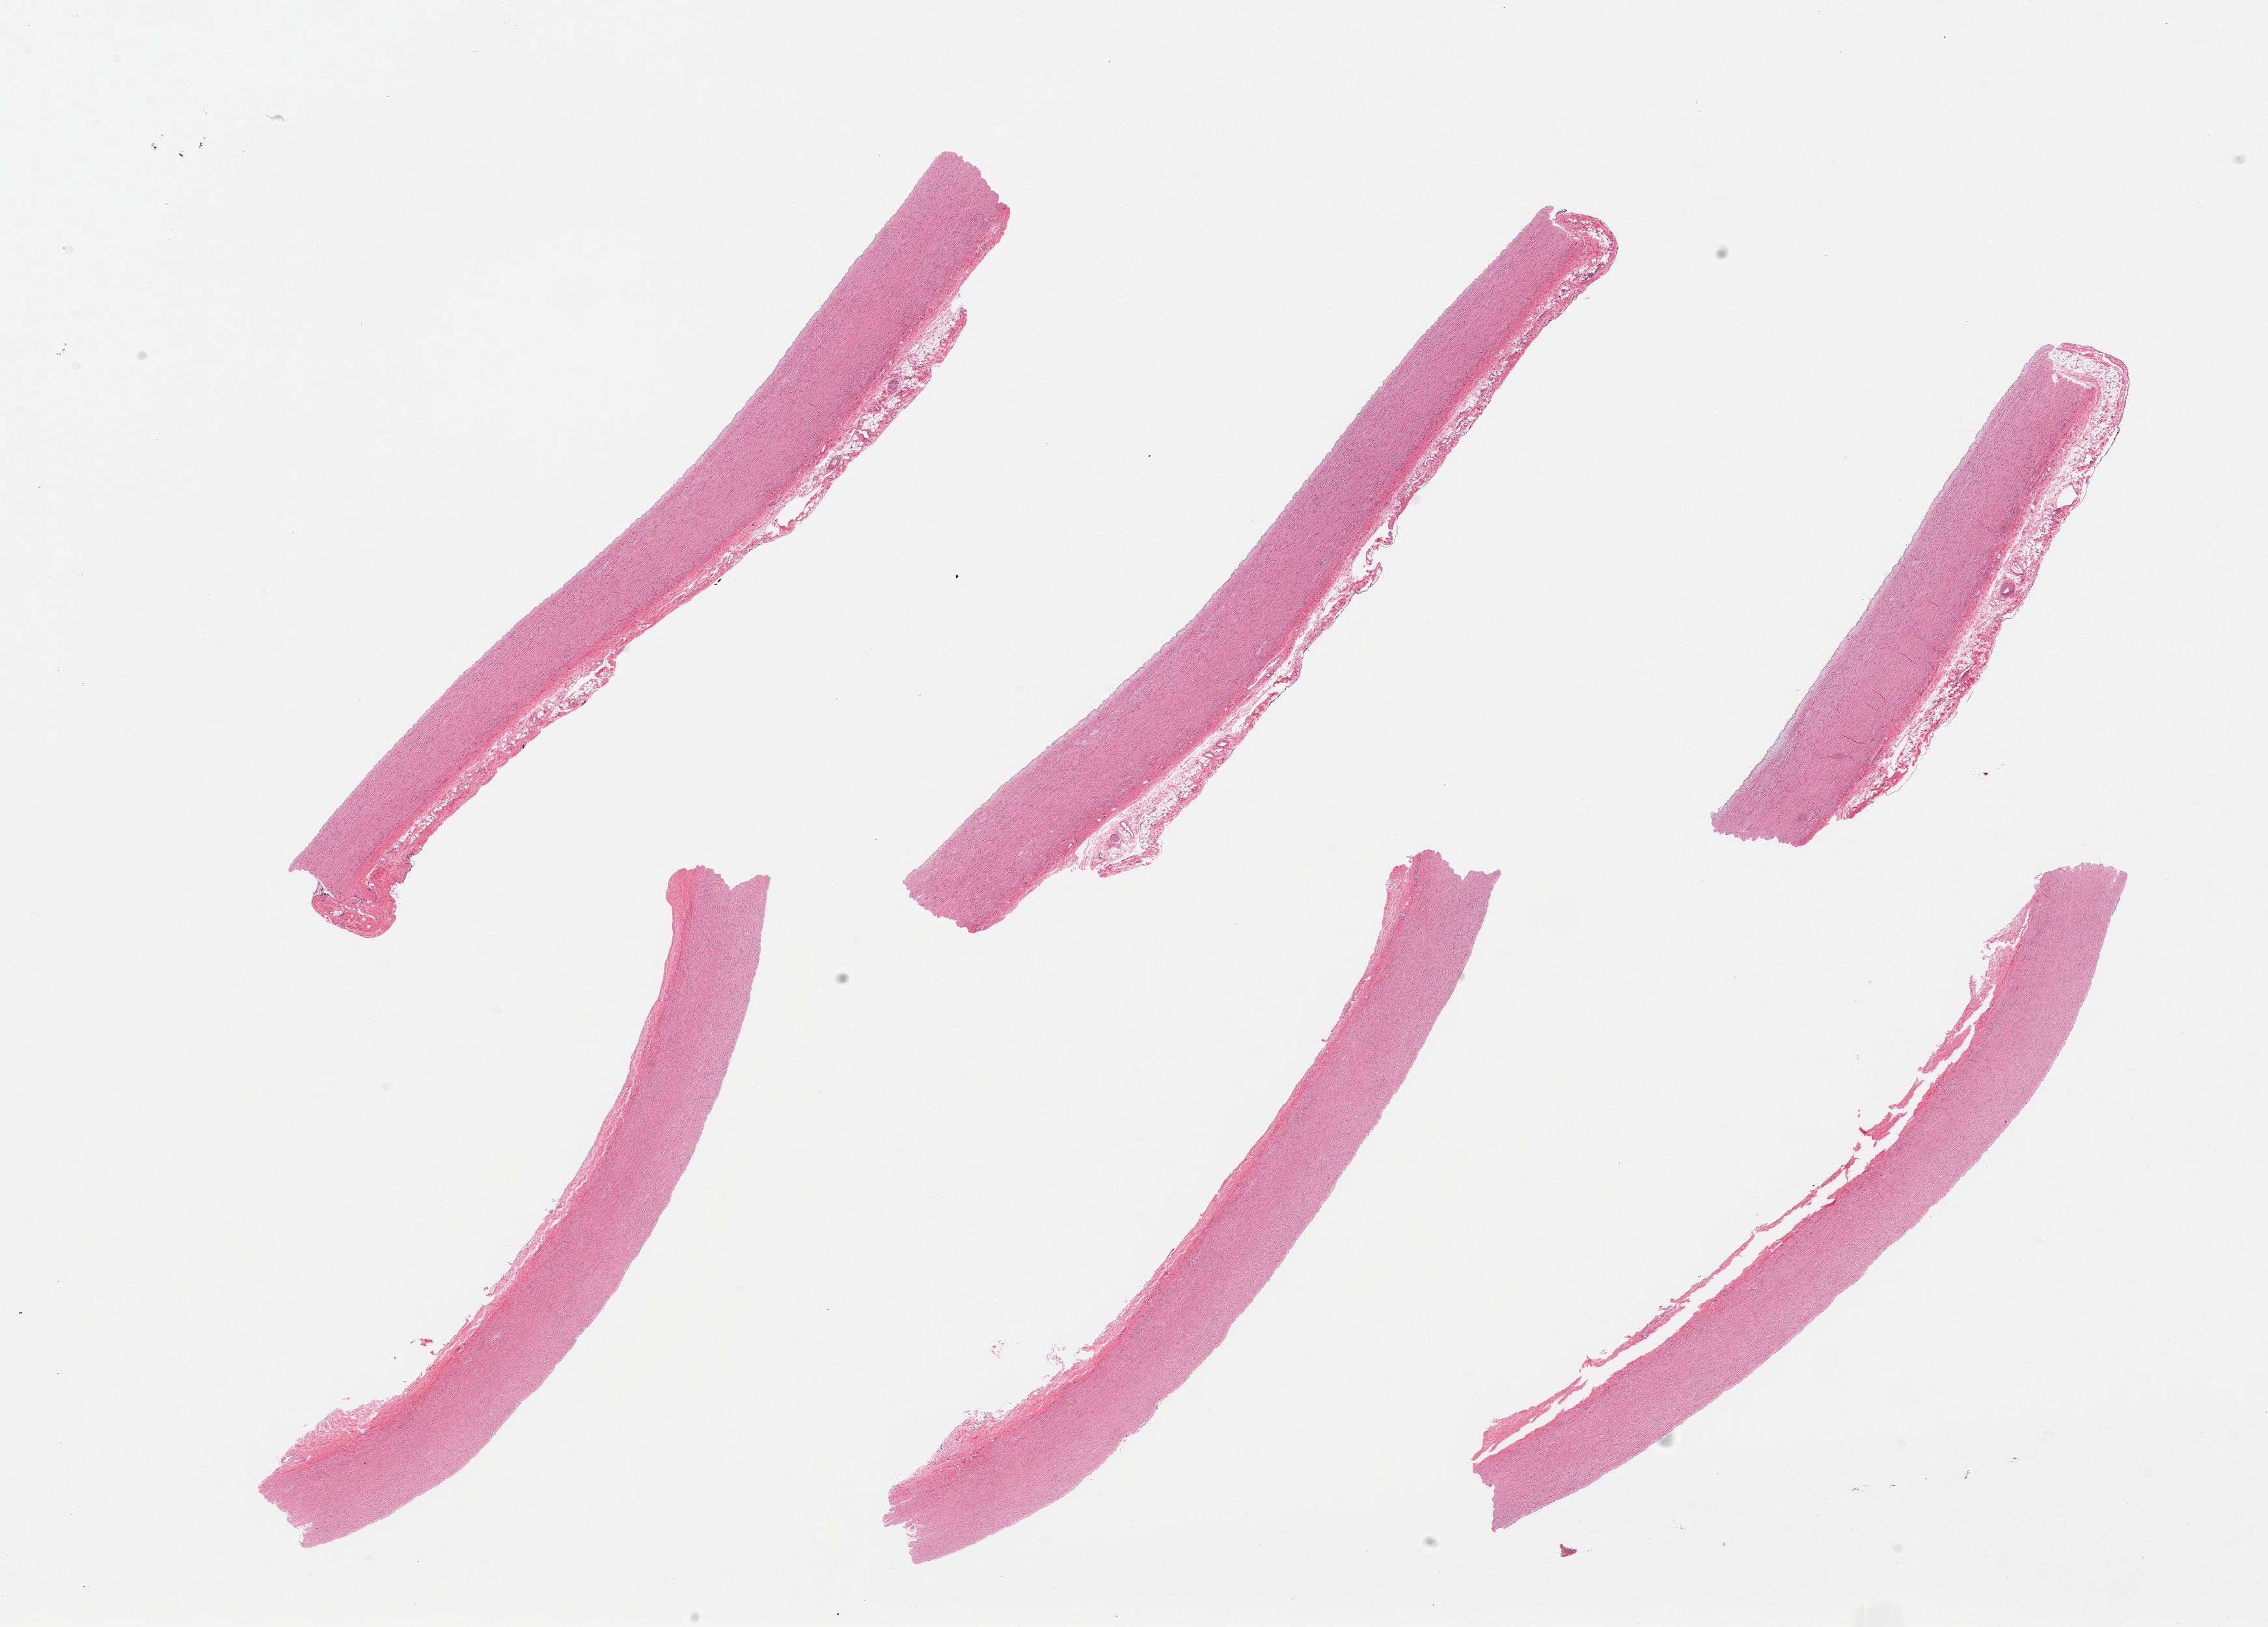
Digitized hematoxylin and eosin (H&E)-stained section — a low-resolution overview of the entire scanned area, about 27.6 x 19.8 mm, PAXgene-fixed paraffin-embedded (PFPE) section, sampled site (target tissue): aorta, tissue donor sample.
Review note (as recorded): 6 pieces, well trimmed.